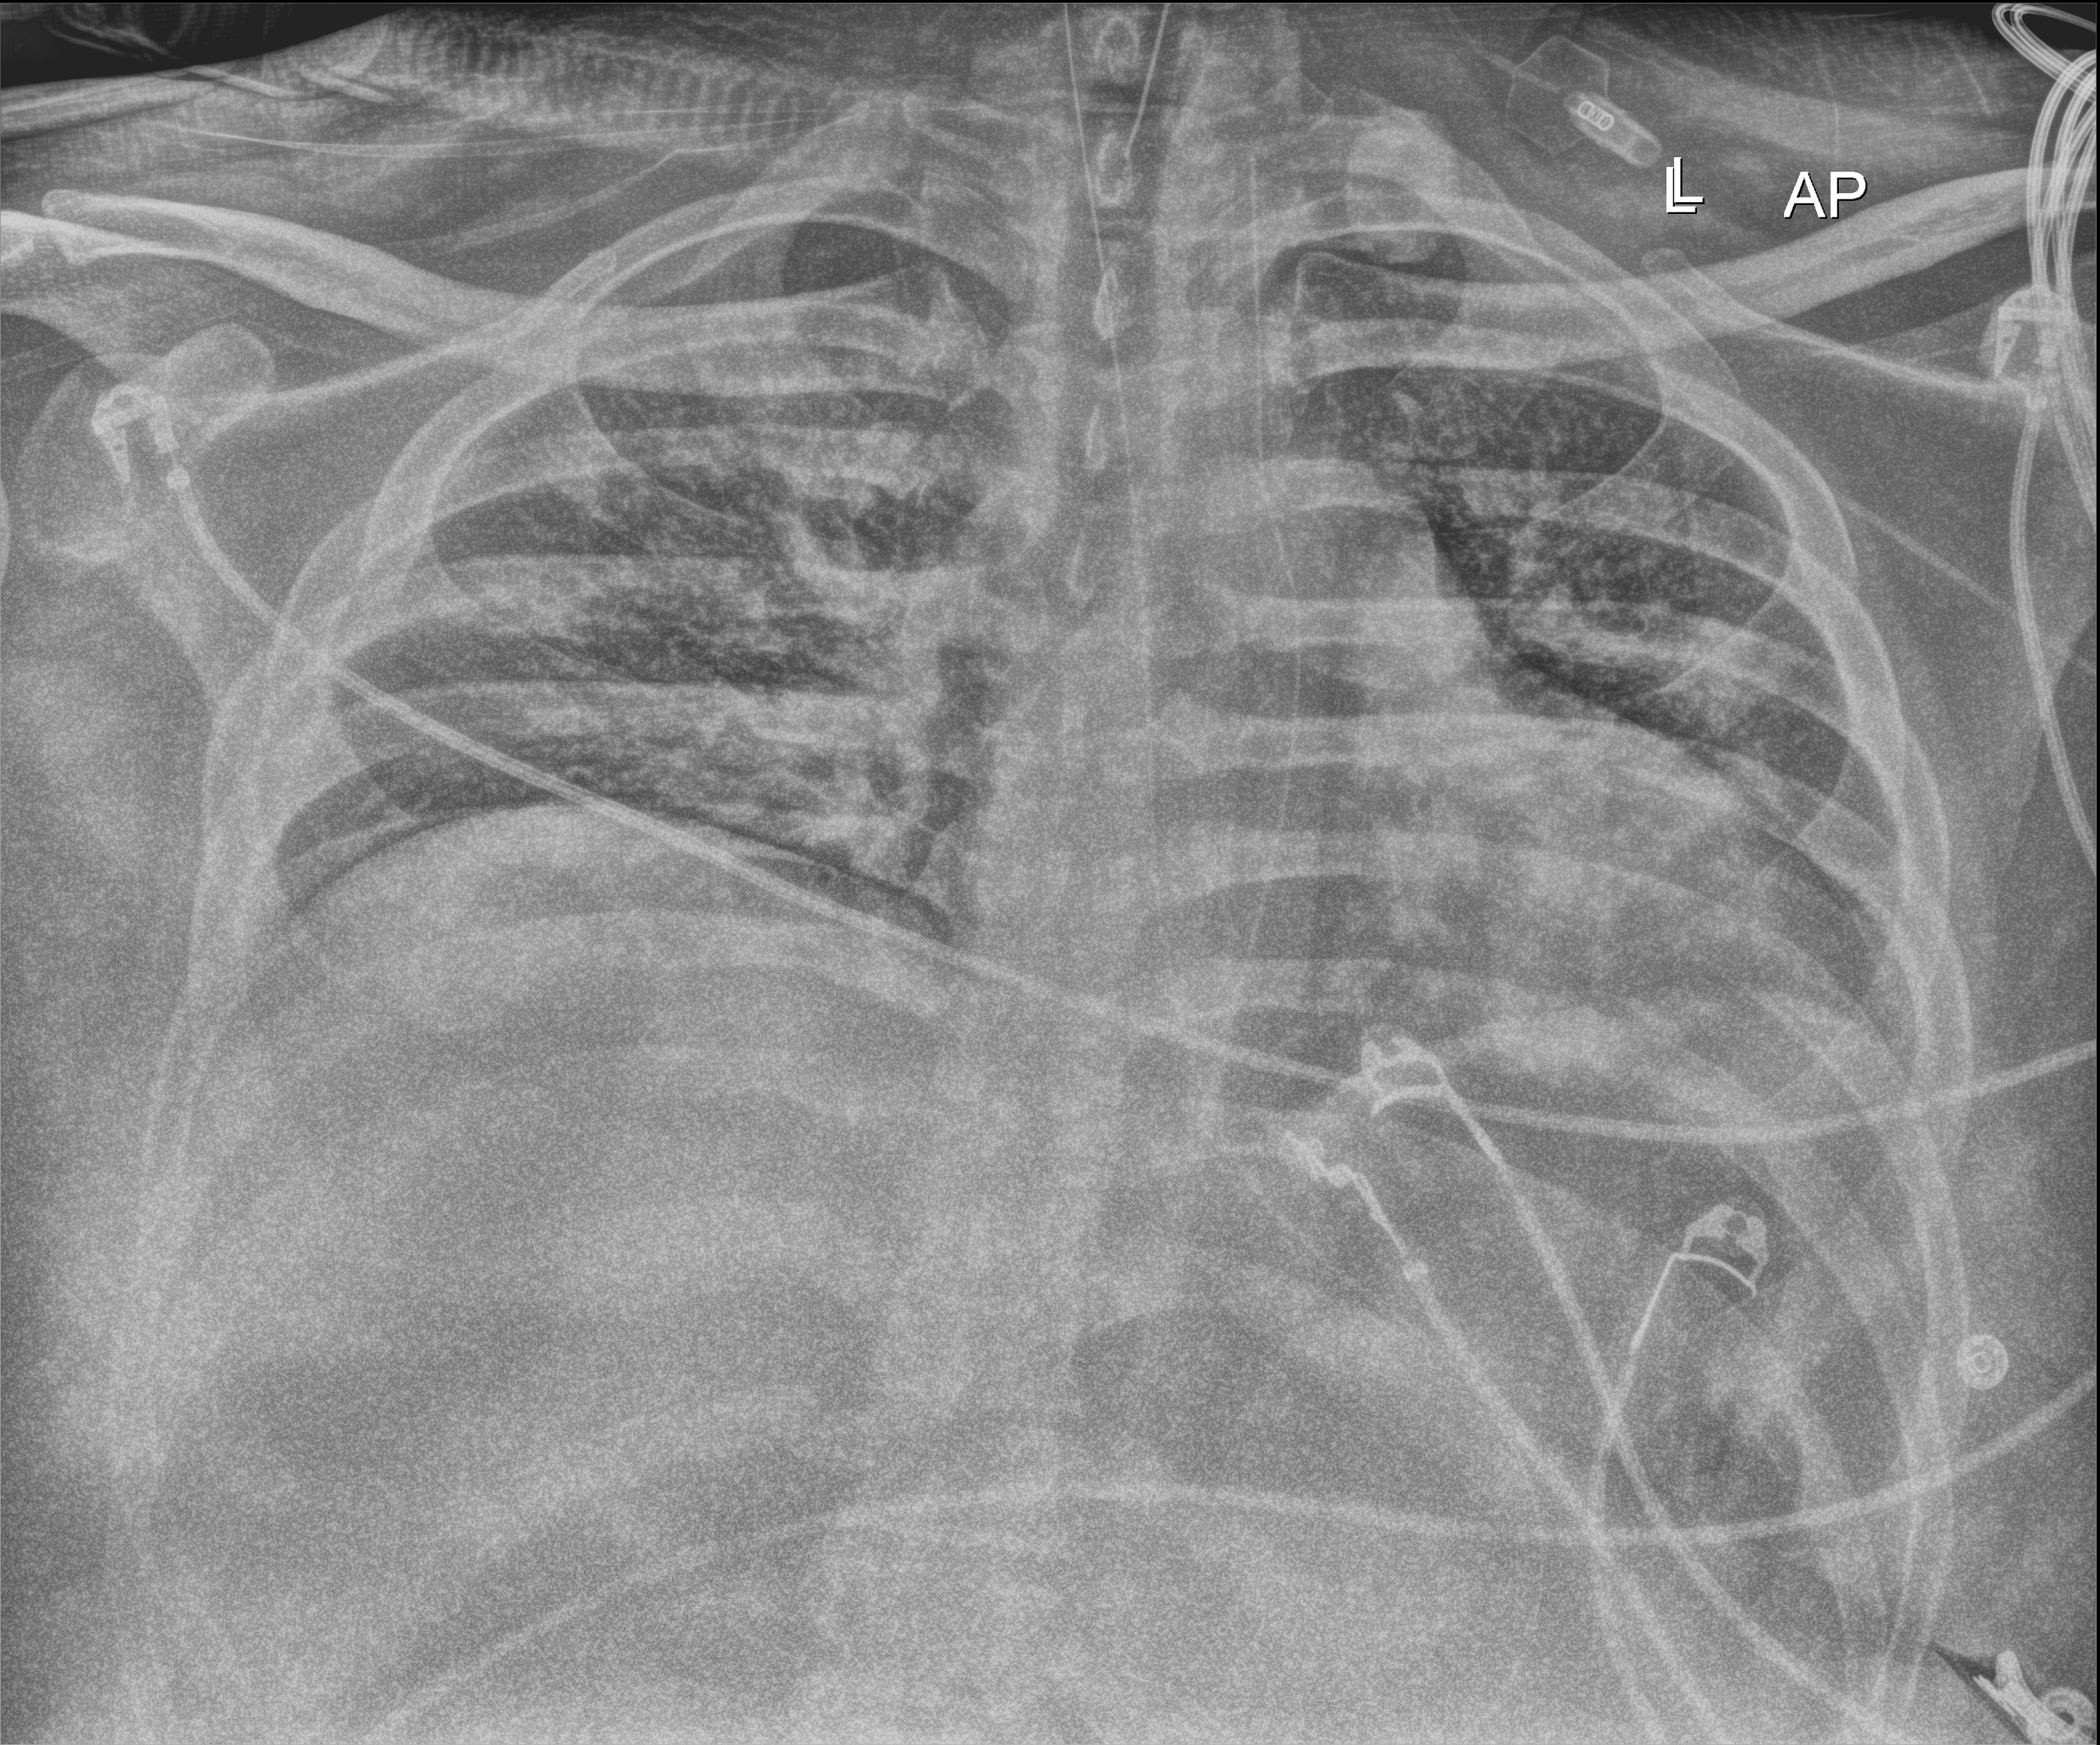
Chest X-ray (portable); anteroposterior (AP) projection. Patient hospitalised with COVID-19; male, aged 18–59 years.
From the hospital-stay record, not from the radiograph (when in the stay this image was taken is not recorded): mechanically ventilated during this hospital stay: yes.